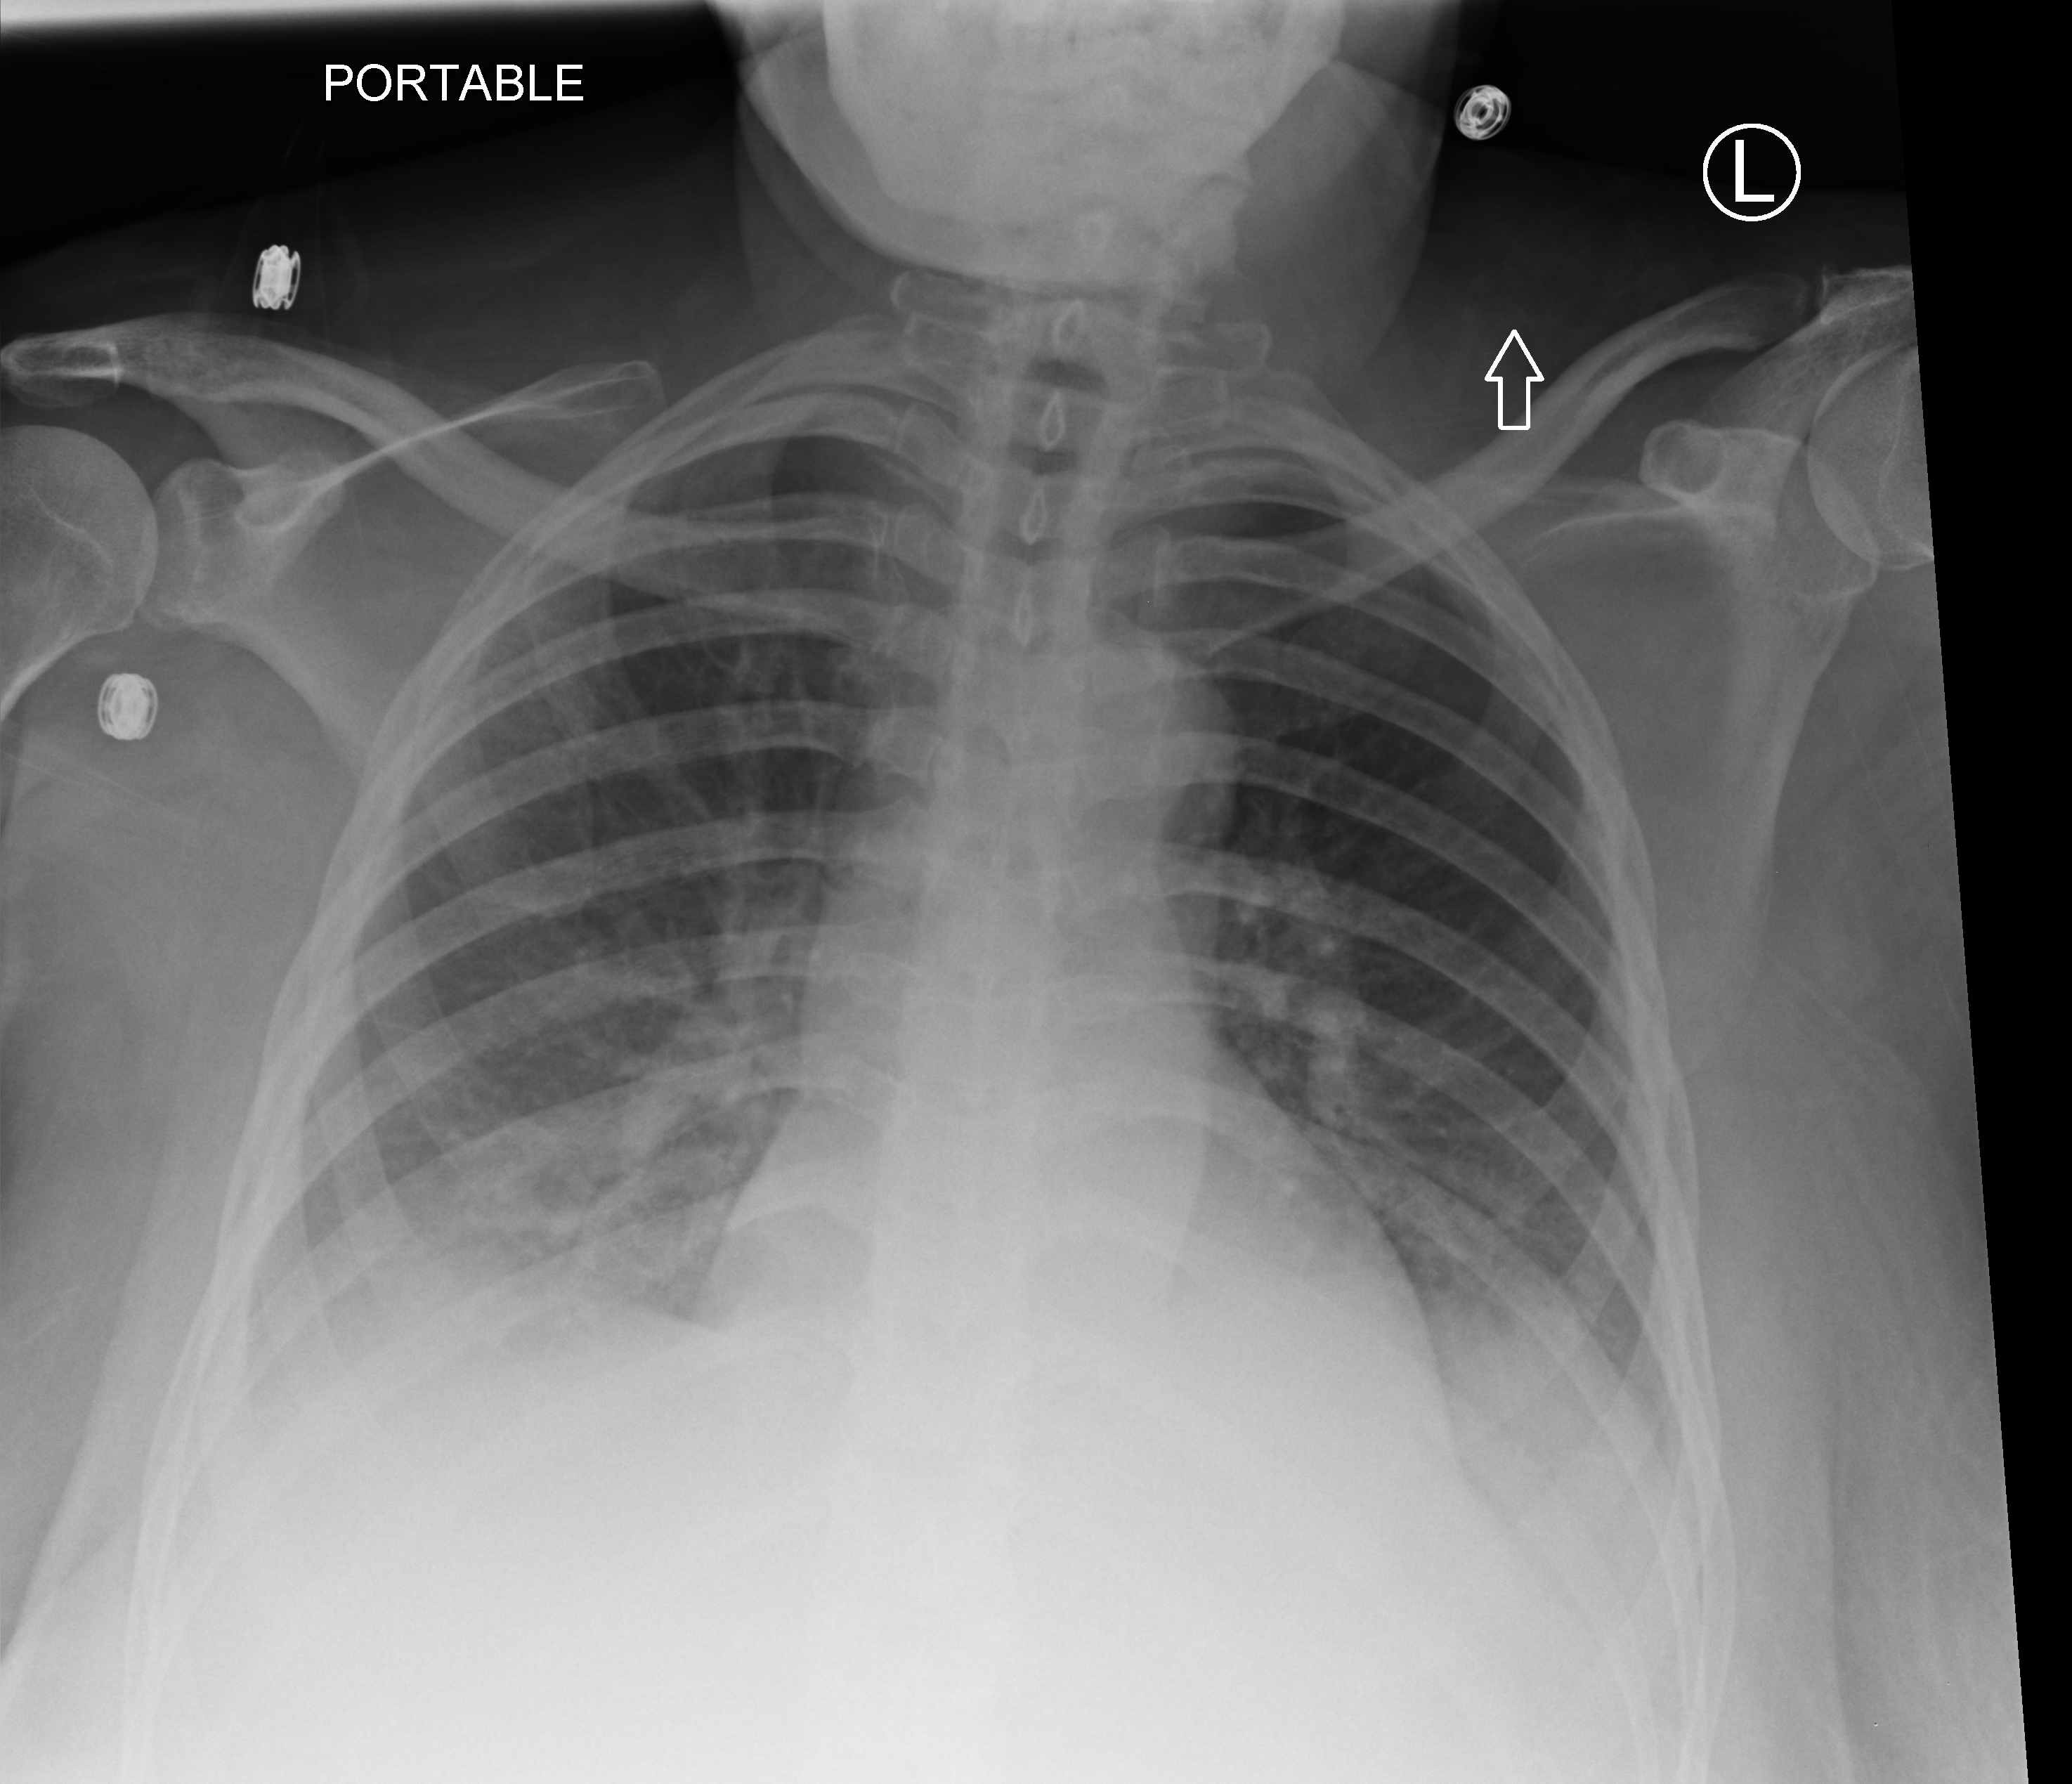
Bedside chest radiograph (computed radiography); anteroposterior (AP) projection. Female patient hospitalised with COVID-19, age 18–59 years.
Admission-level facts for this patient (not findings on this image; timing relative to this image not recorded):
- COPD (admission record): no
- mechanically ventilated during this hospital stay: no